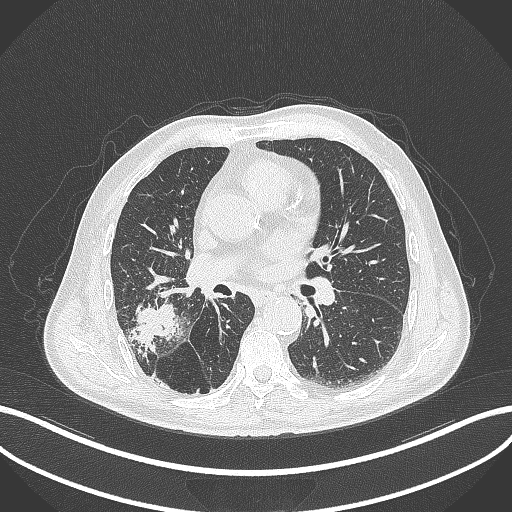
Chest CT, one axial slice; slice 220 of 429 in the series (ordered by position); 120 kVp; lung window (W 1500 / L -600 HU); 1 mm slice thickness; 512 × 512 image matrix. Patient: male, 72 years. From the clinical record (not read from this slice): clinical TNM (as recorded): T3 N2 M0.
Annotated regions visible in this slice (bounding box drawn by a radiologist):
- lung tumour (recorded histology: adenocarcinoma): bounding box [x1, y1, x2, y2] px = [122, 301, 182, 355]